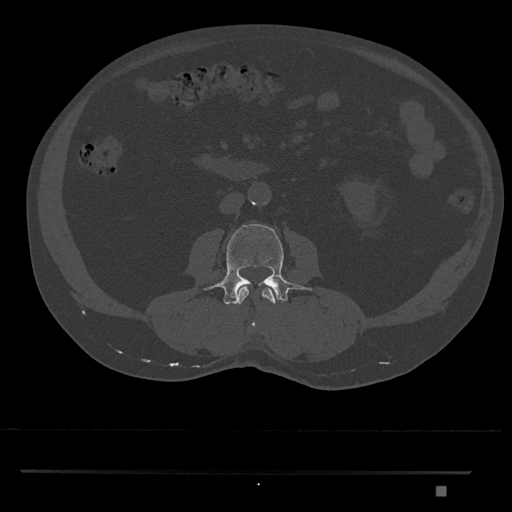
CT including the spine, one axial slice. Position 699 of 1134 along the scan axis. 120 kVp. Bone window (W 1800 / L 400 HU). 0.5 mm slice thickness. 512 × 512 image matrix, field of view 429 × 429 mm. Male patient, age 65 years. Case-level facts recorded for this patient, not image findings: primary cancer: prostate.
Outlined on this slice (semi-automatic segmentation, software-assisted and operator-edited):
- L2 vertebra: bounding box (x1, y1, x2, y2) in pixels: (237, 286, 276, 328)
- L3 vertebra: (204, 224, 311, 305)